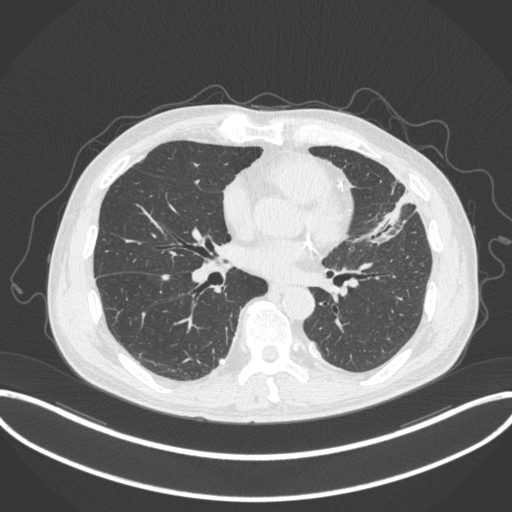
Chest CT, one axial slice; position 150 of 382 along the scan axis; reconstruction kernel B31f; lung window (W 1500 / L -600 HU); 1 mm slice thickness; 512 × 512 image matrix, field of view 415 × 415 mm. Patient: male, 64 years. From the clinical record (not read from this slice): clinical TNM (as recorded): T4 N1 M0; histopathological grade: G3.
Annotated regions visible in this slice (bounding box drawn by a radiologist):
- lung tumour (recorded histology: adenocarcinoma): bounding box <365,189,420,252> (left, top, right, bottom; pixels)